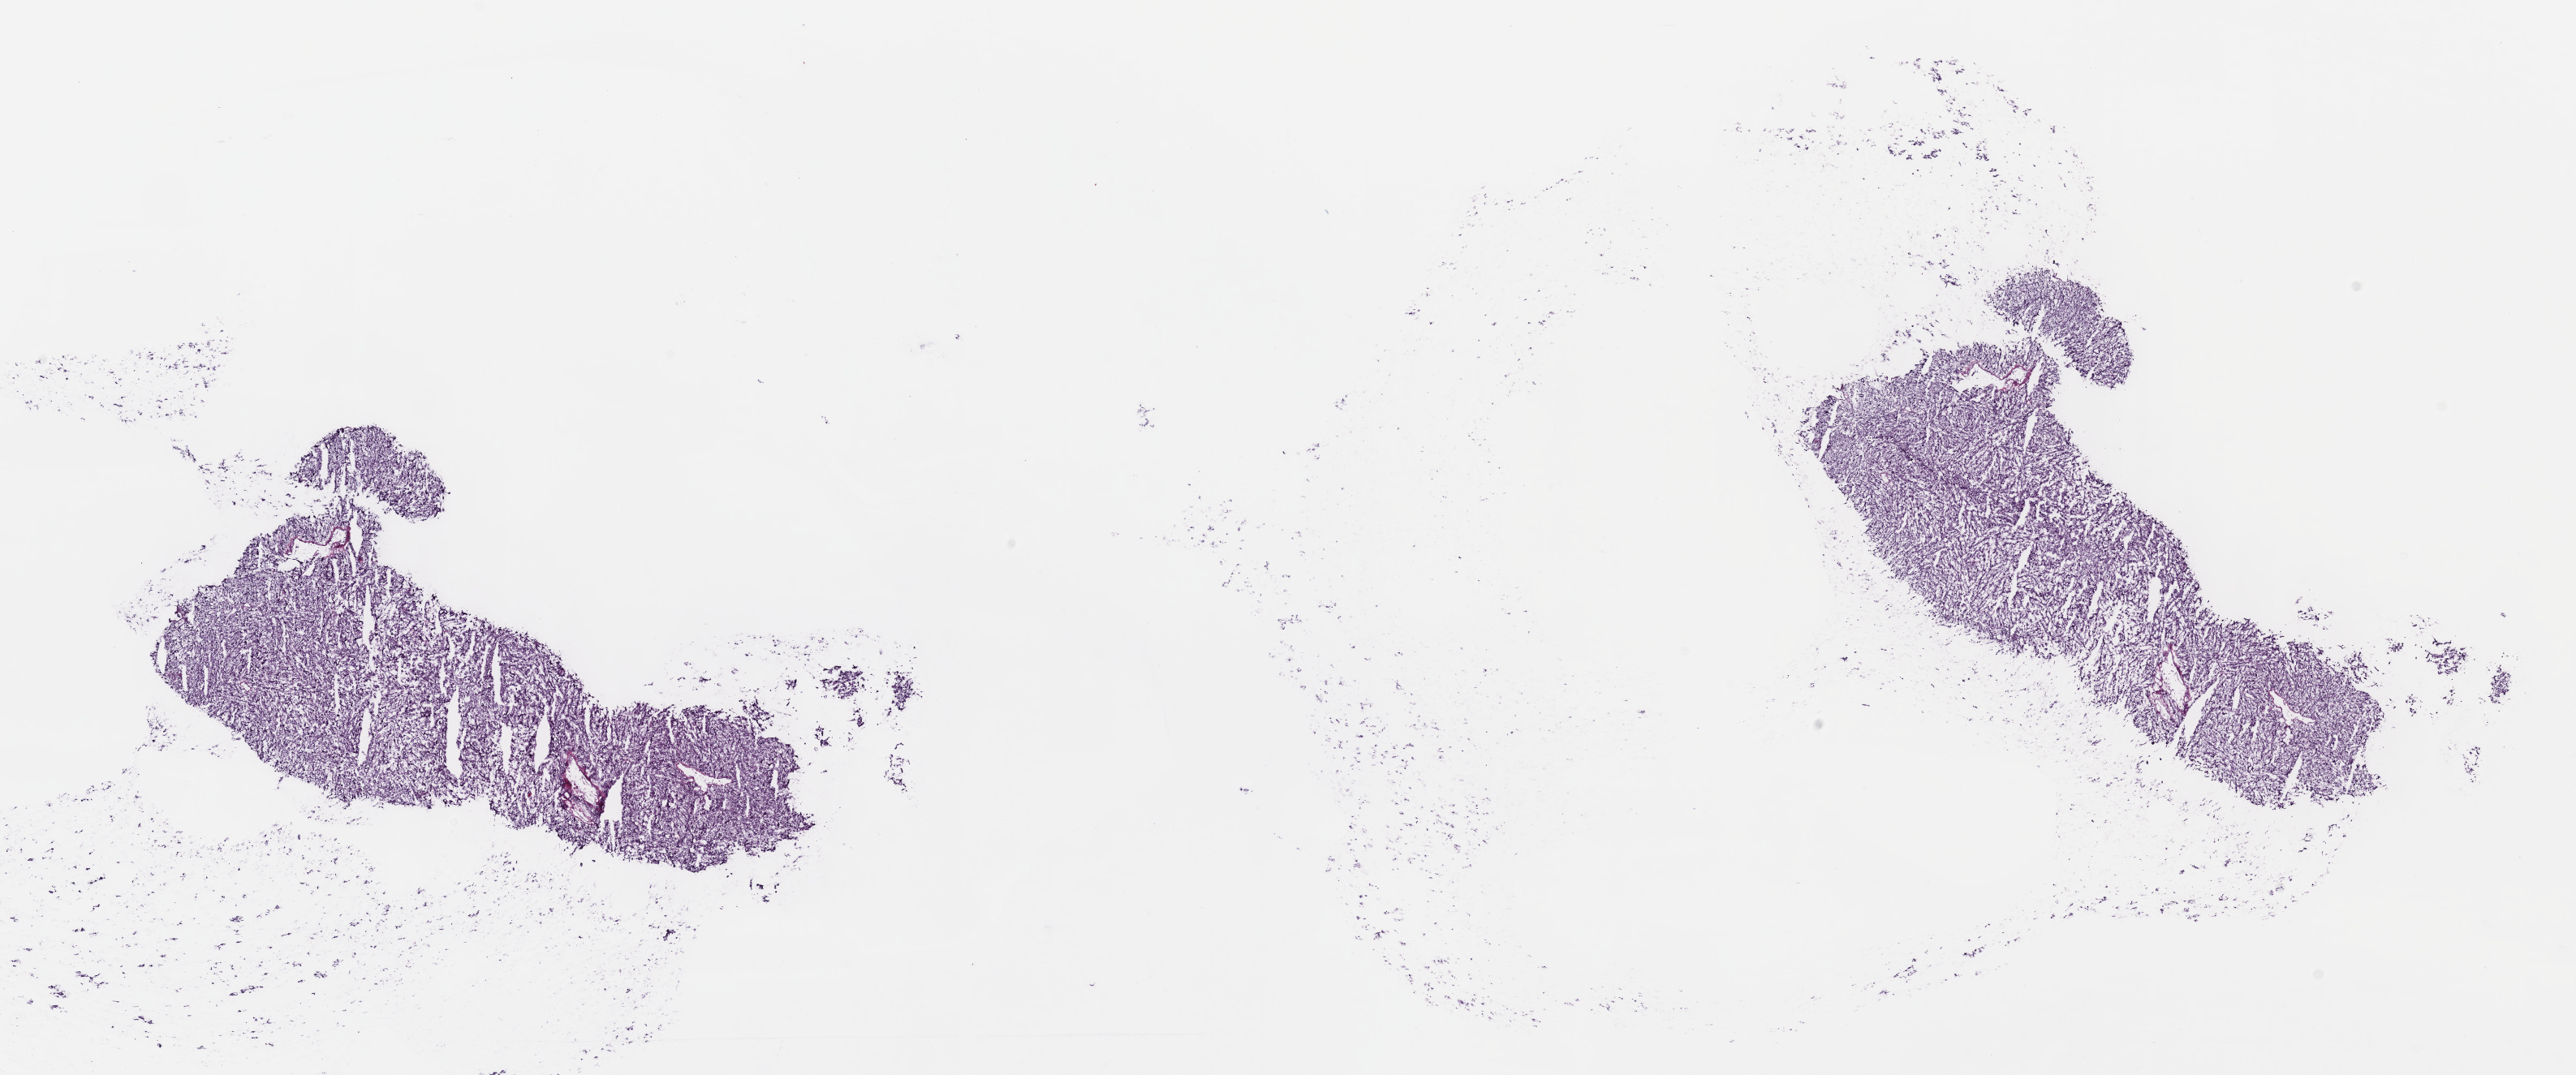
H&E-stained whole-slide image — low-resolution overview of the scanned area, about 25.7 x 10.7 mm, frozen section, sample: primary tumour, adrenal gland. Female patient; age at initial diagnosis 55 years. Slide review estimates, as recorded: tumour cells 100%, tumour nuclei 80%, normal cells 0%, stromal cells 0%, necrosis 0%. Inflammatory infiltration, as recorded: lymphocyte infiltration 1%, monocyte infiltration 0%, neutrophil infiltration 0%.
Laterality: left. Histologic diagnosis: Pheochromocytoma, NOS.